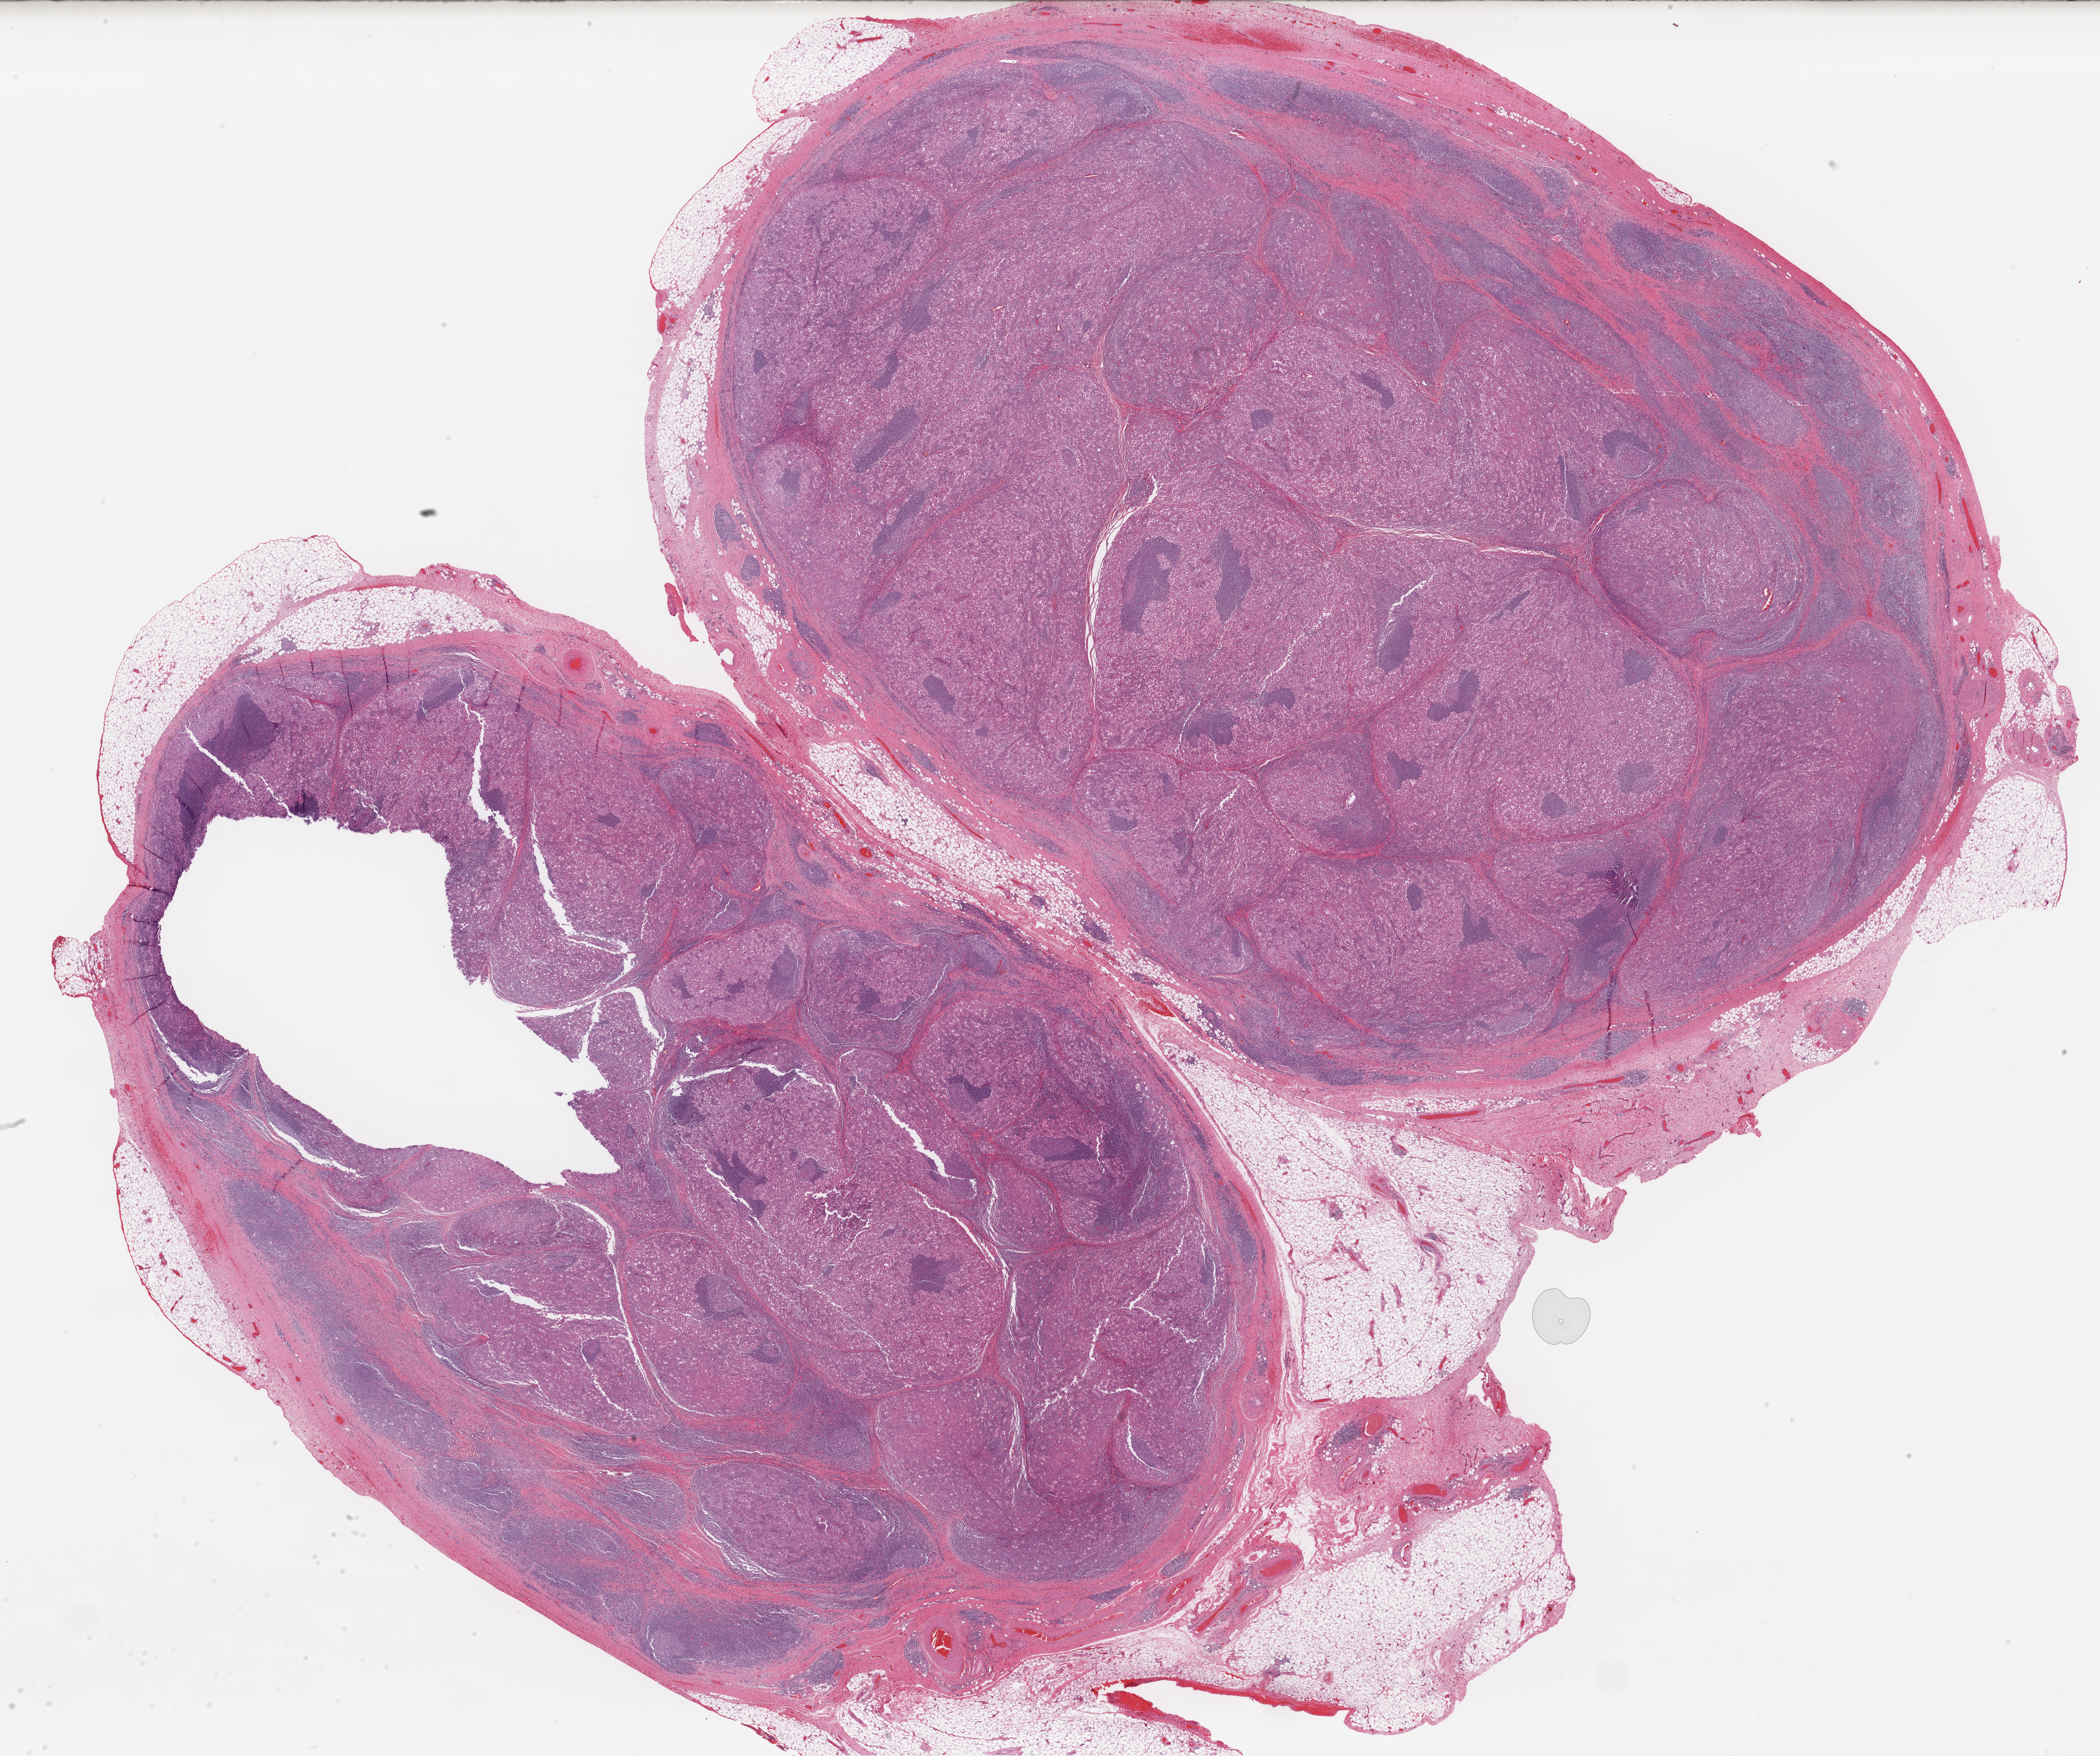
Digitized H&E-stained tissue section (whole slide), a low-resolution overview of the entire scanned area, about 28.0 x 23.4 mm. Formalin-fixed paraffin-embedded (FFPE) diagnostic section. Sample: primary tumour, skin. Patient: female, age at initial diagnosis 43 years.
Pathologic diagnosis: Malignant melanoma, NOS.